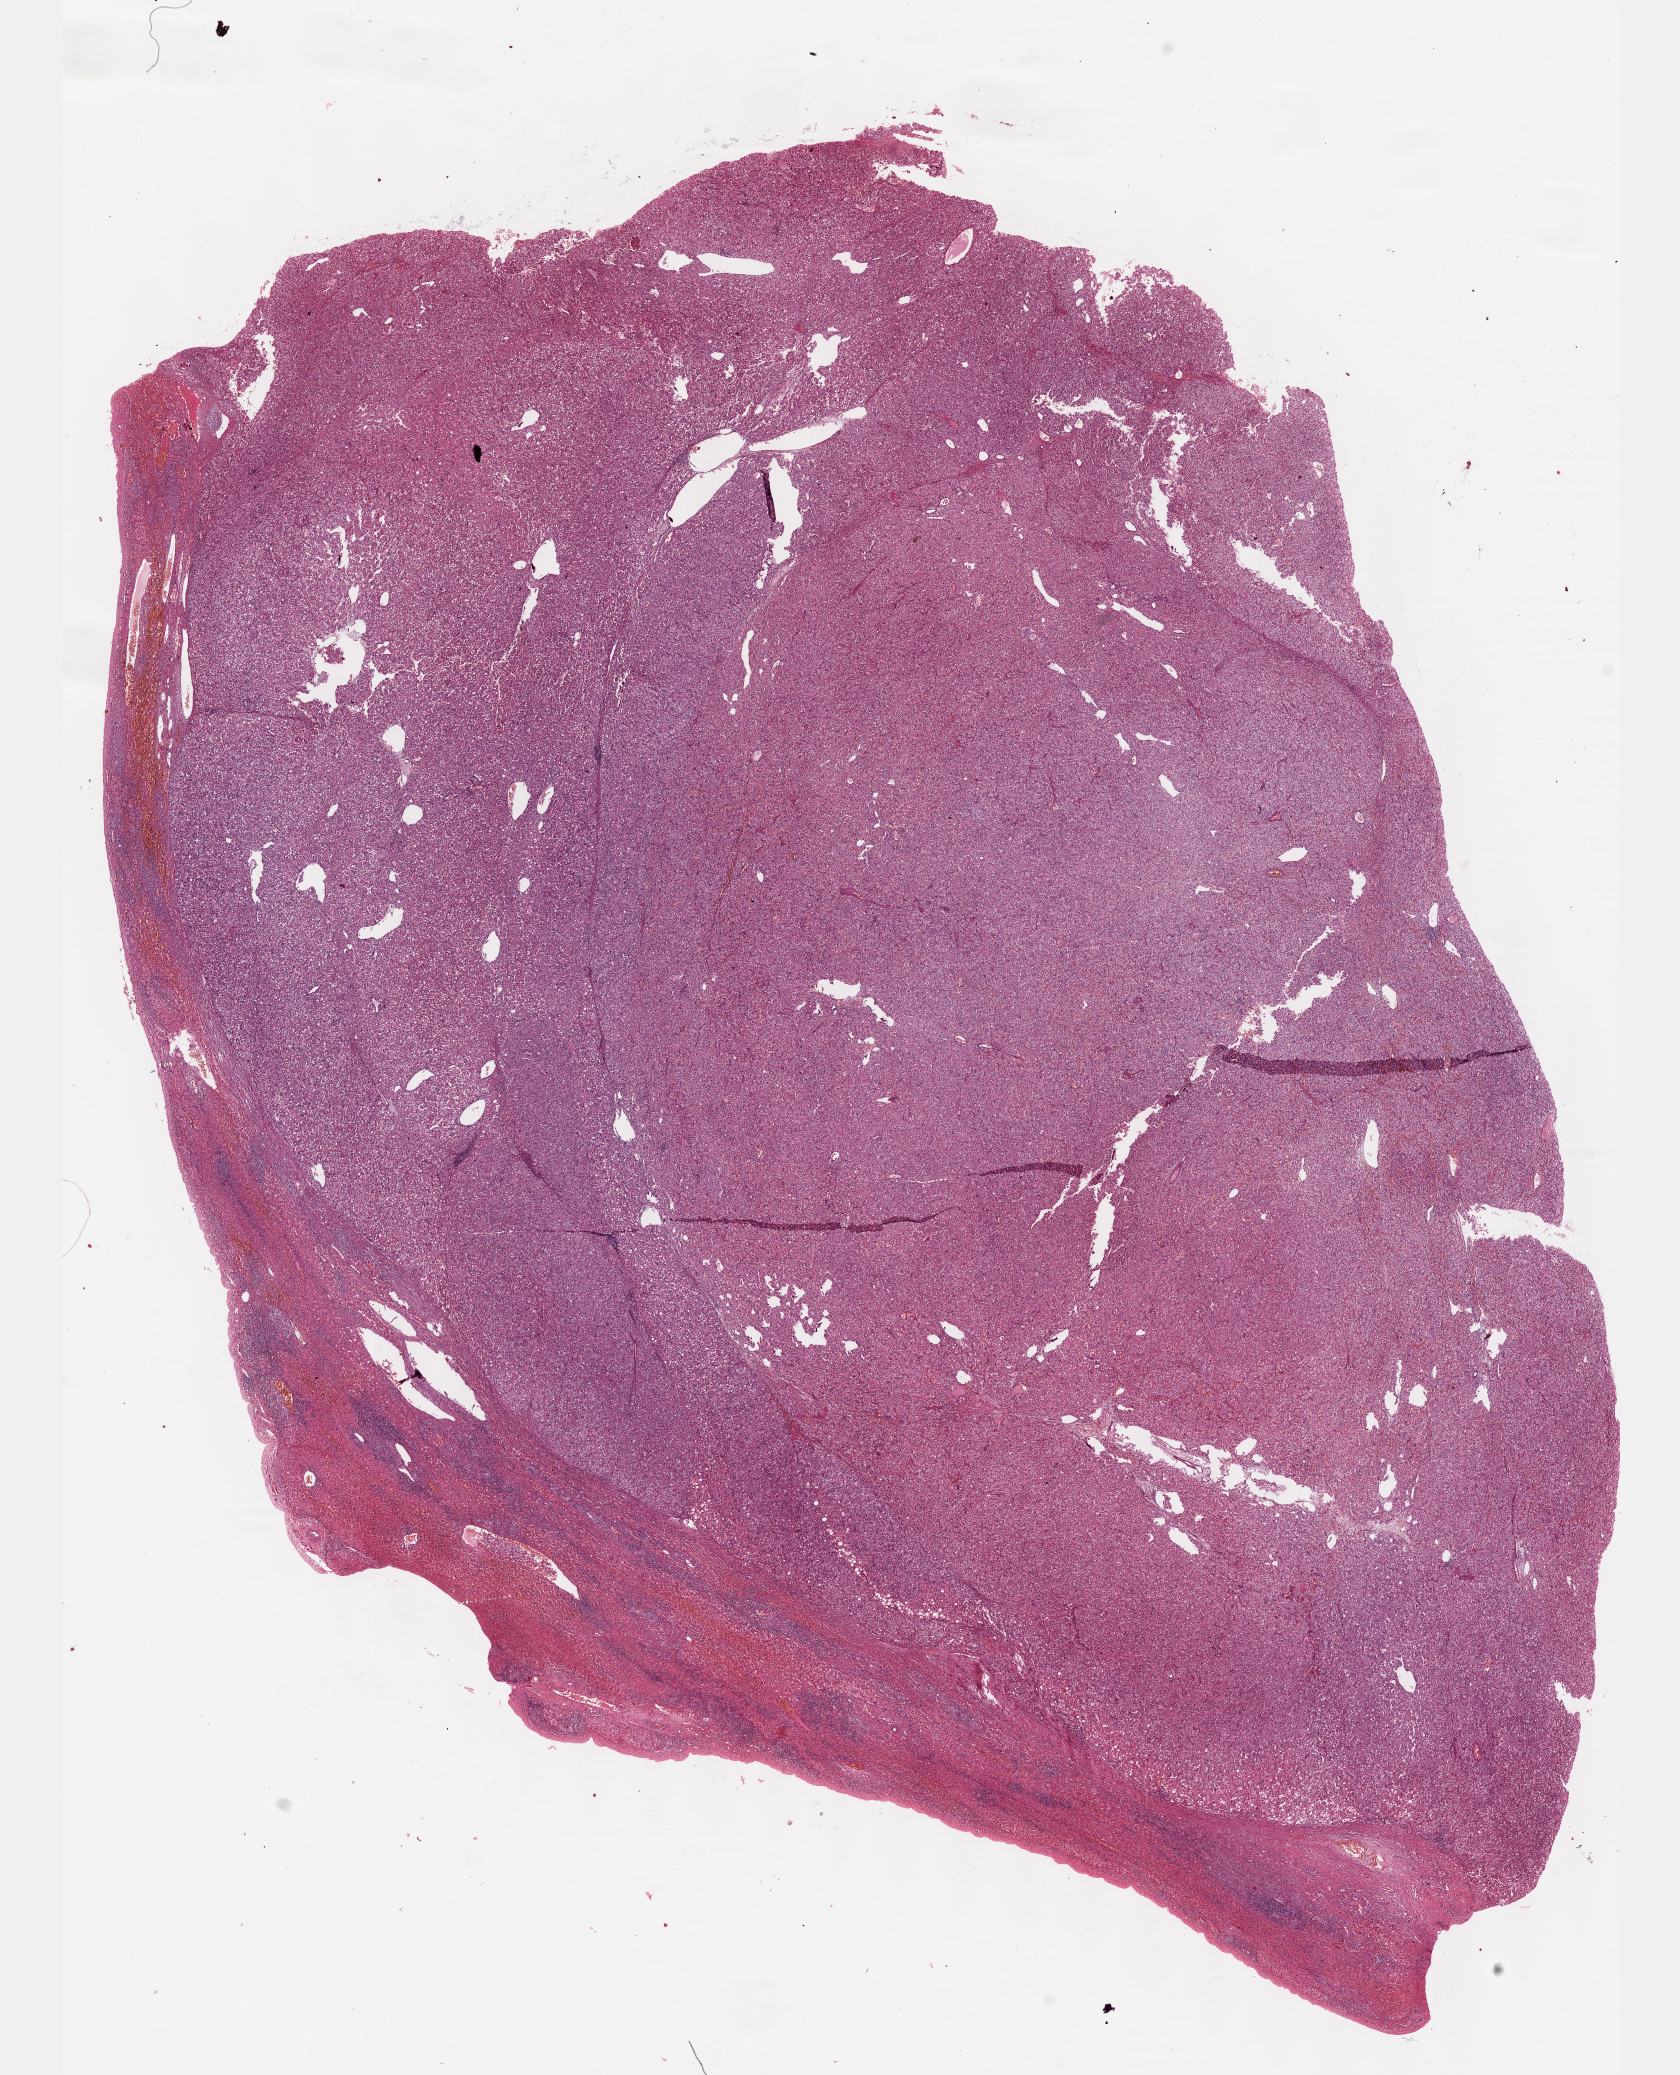
Digitized Hematoxylin and eosin (H&E) stained tissue section (whole slide) — whole scanned area (about 13.6 x 16.8 mm) shown as a low-resolution overview, FFPE section, sample: primary tumour, liver. Male patient; age at initial diagnosis 55 years.
Histologic diagnosis: Hepatocellular carcinoma, NOS.